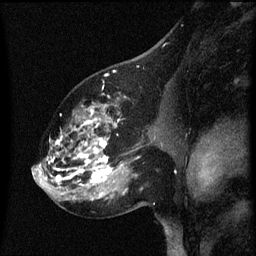
Breast MRI (dynamic contrast-enhanced), one sagittal slice; slice 35 of 60 in the series (ordered by position); dynamic contrast-enhanced series, image 2 of 3 at this slice position (ordered by acquisition); 1.5 T; TE 4.2 ms, TR 8 ms; 2 mm slice thickness; 256 × 256 image matrix, field of view 200 × 200 mm. Patient: female, 60 years.
Structures marked on this image (semi-automatic segmentation, software-assisted and operator-edited):
- analysis volume of interest (the breast-tissue region the enhancement analysis was run in; not a lesion): bounding box (x1, y1, x2, y2) in pixels: (49, 98, 158, 197)
- tumour enhancement mask (voxels above the 70 % enhancement threshold inside the analysis volume of interest): (49, 108, 139, 195)